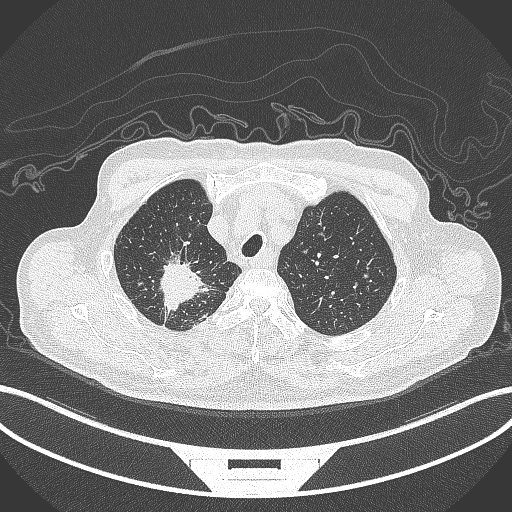
Chest CT, one axial slice; slice 317 of 407 in the series (ordered by position); reconstruction kernel B70f; 120 kVp; lung window (W 1500 / L -600 HU); 1 mm slice thickness; 512 × 512 image matrix, field of view 400 × 400 mm. Patient: male, 69 years. From the clinical record (not read from this slice): clinical TNM (as recorded): T1c N1 M1.
Annotated regions visible in this slice (bounding box drawn by a radiologist):
- lung tumour (recorded histology: adenocarcinoma): box from (x=151, y=253) to (x=212, y=316) px